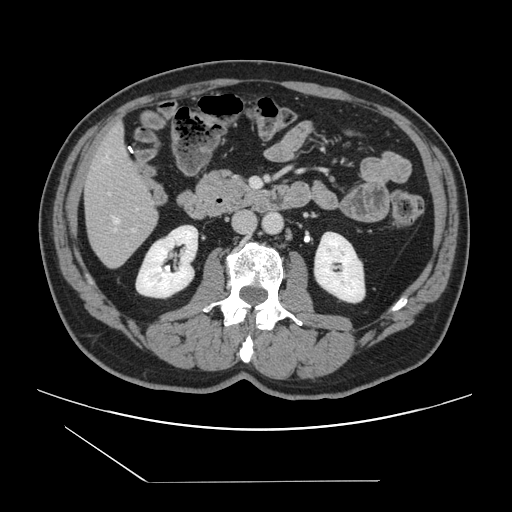
Contrast-enhanced abdominal CT, one axial slice. Position 44 of 157 along the scan axis. 120 kVp. Intravenous contrast given. Soft-tissue window (W 400 / L 40 HU). 2.5 mm slice thickness. 512 × 512 image matrix. Male patient, age 61 years. From the clinical record (not read from this slice): diagnosis: colorectal cancer liver metastases, imaged before liver resection; multiple liver metastases: yes; largest metastasis: 5.5 cm.
Outlined on this slice (outlined manually by an expert reader):
- hepatic veins: box from (x=113, y=217) to (x=119, y=230) px
- liver: (x=85, y=127)–(x=158, y=267)
- planned liver remnant (the part of the liver to remain after resection): (x=85, y=128)–(x=155, y=219)
- portal vein (with intrahepatic branches): (x=109, y=194)–(x=136, y=231)